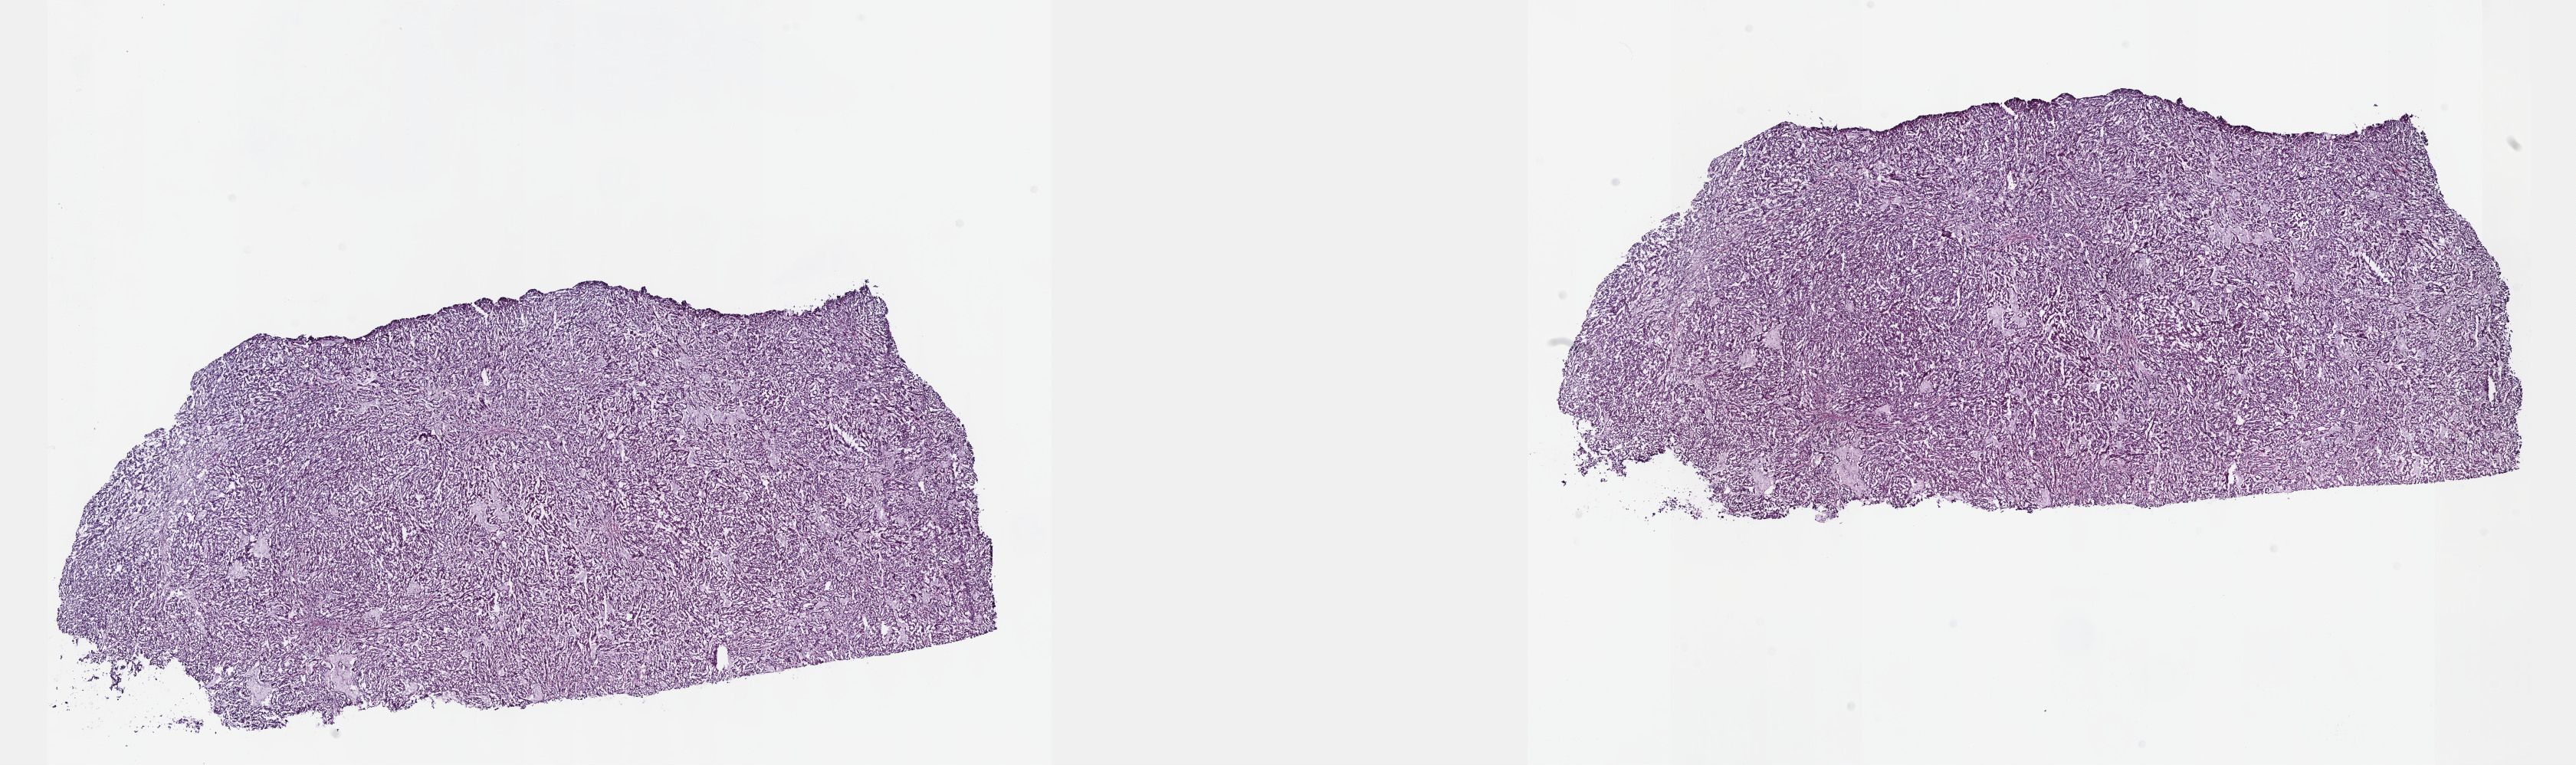
Hematoxylin and eosin (H&E) stained whole-slide image — shown as a low-resolution overview of the whole scanned area (about 27.2 x 8.1 mm, slide scanned at 40x); frozen section from the top of the tissue portion; kidney, primary tumour sample. Male patient; age at initial diagnosis 65 years. Composition of this section per pathologist review: tumour cells 100%, tumour nuclei 93%.
Pathologic diagnosis: Papillary adenocarcinoma, NOS.